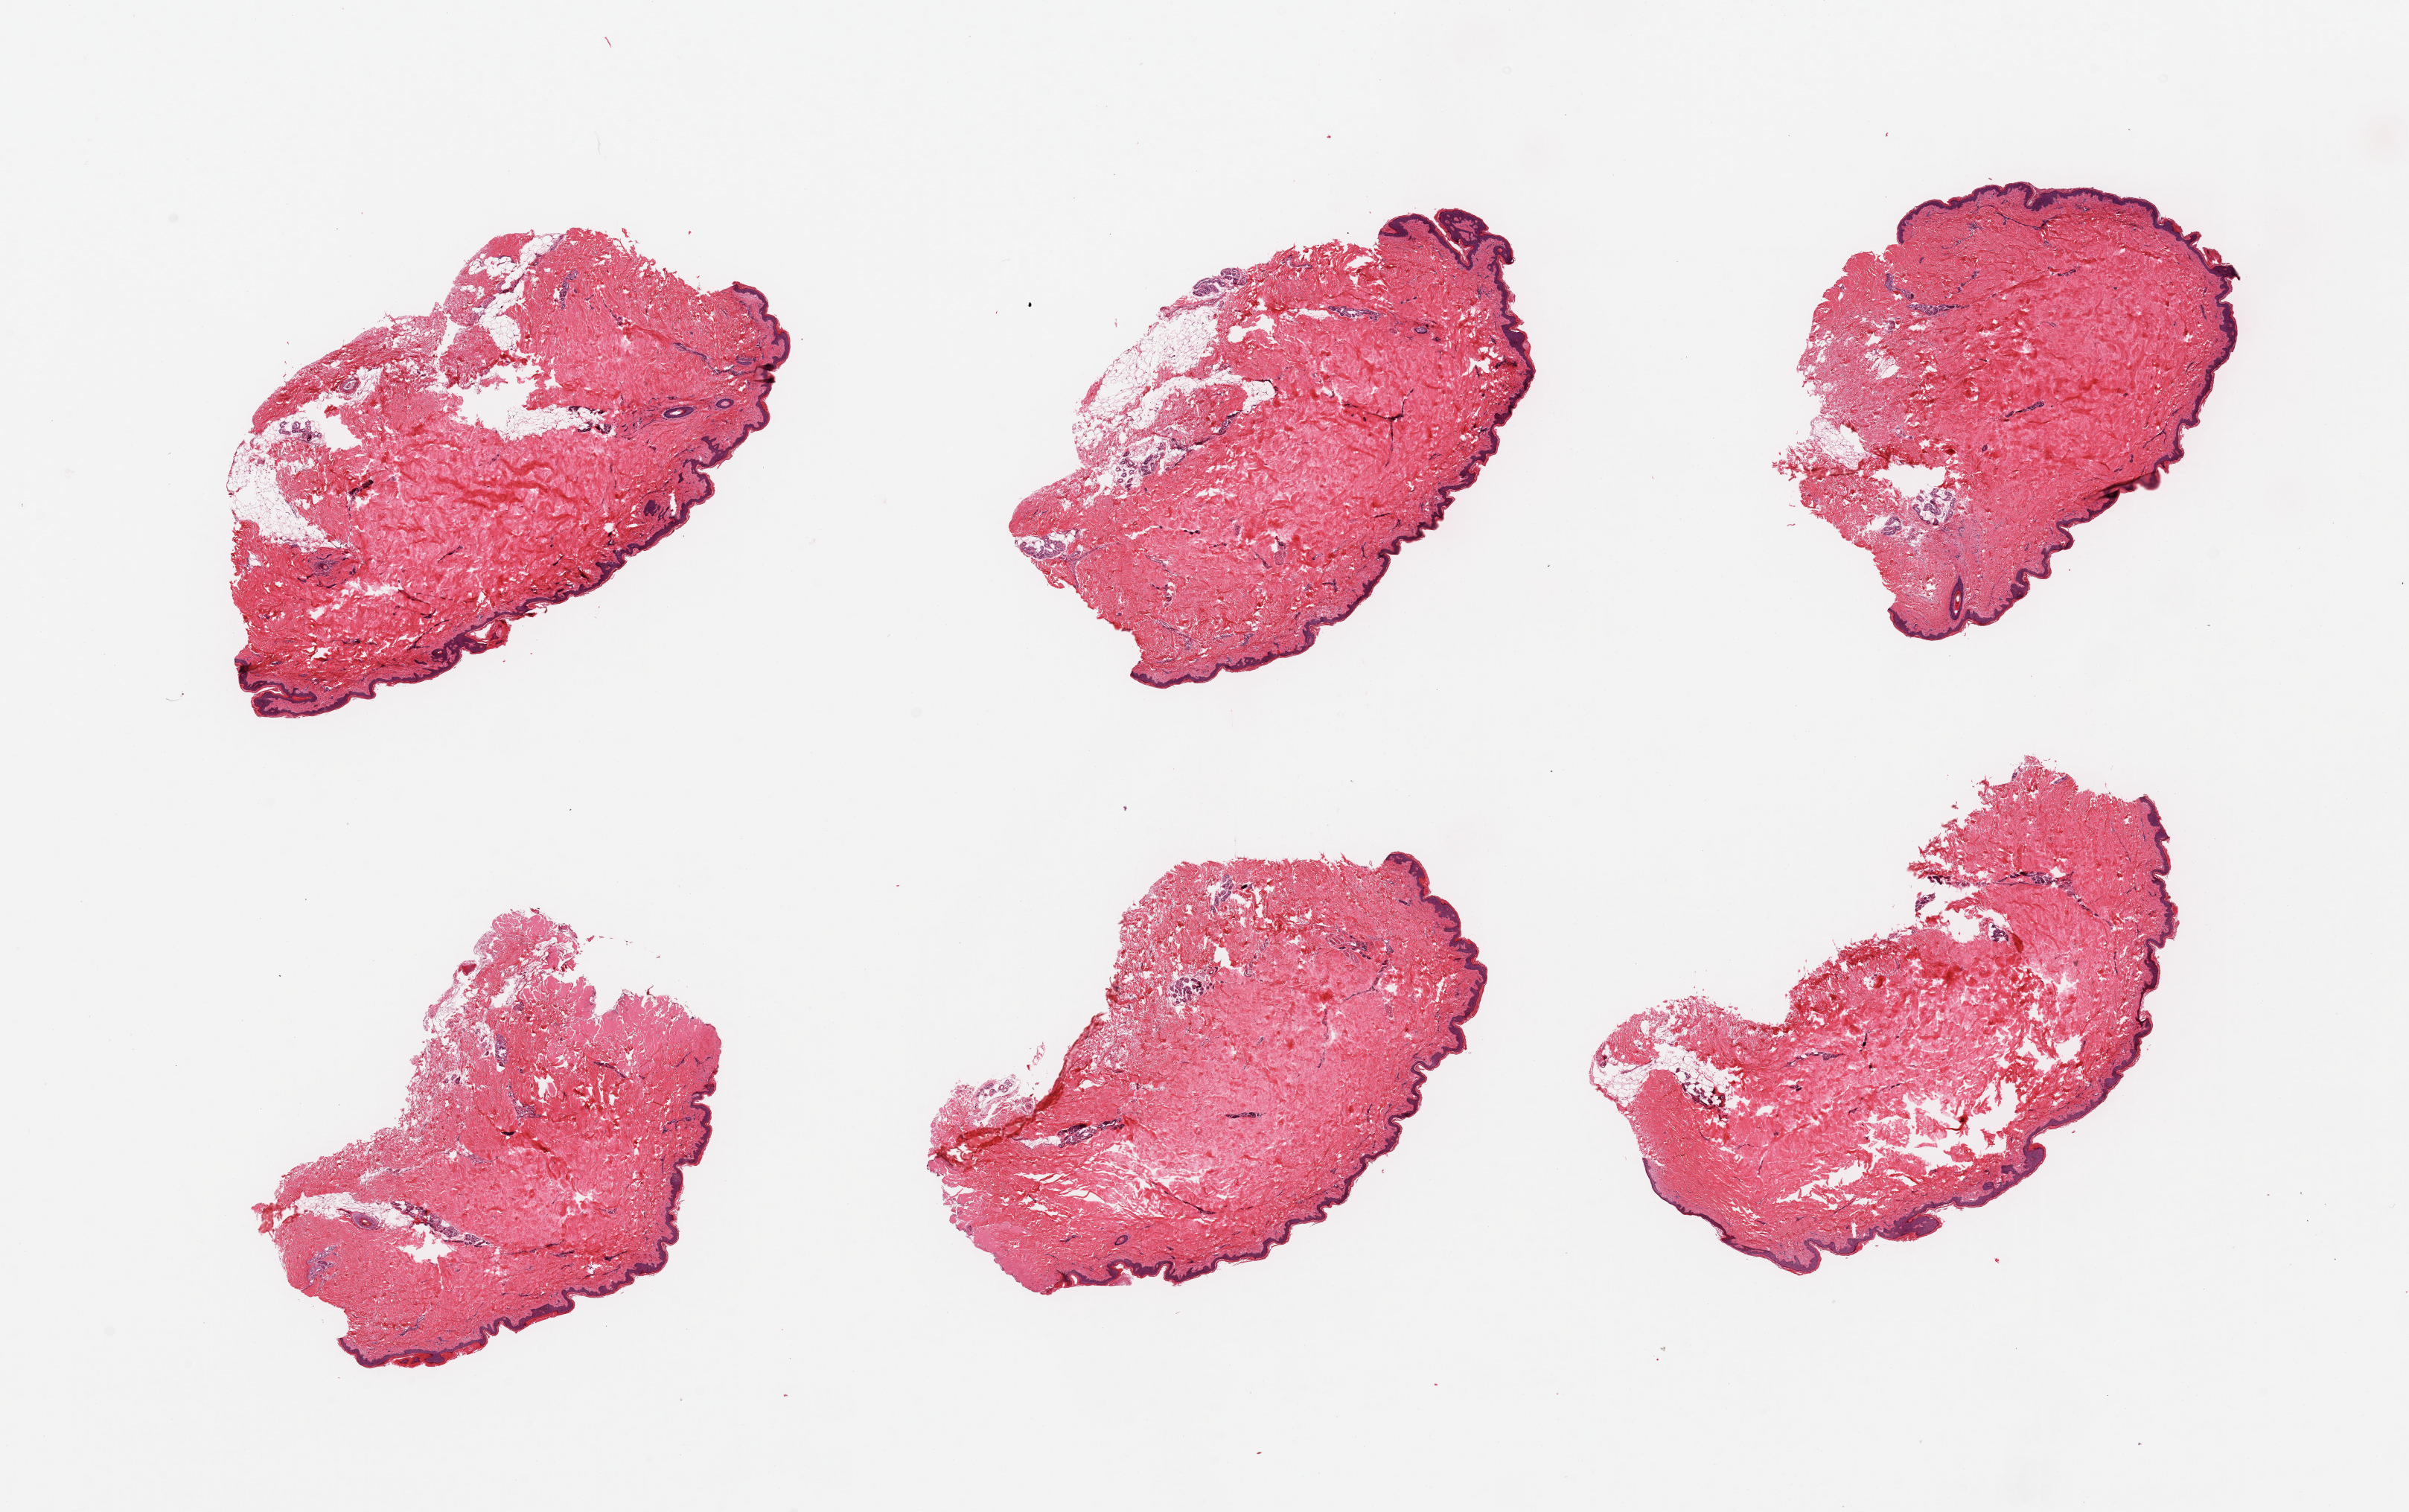
Haematoxylin and eosin whole-slide image, shown as a low-resolution overview of the whole scanned area (about 25.6 x 16.1 mm), PAXgene-fixed, paraffin-embedded tissue, section of skin of suprapubic region (target tissue), donor tissue sample.
Review note (as recorded): 6 pieces; well trimmed; 5-10% dermal fat.